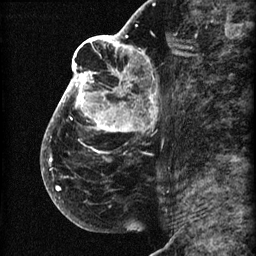
Breast MRI (dynamic contrast-enhanced), one sagittal slice. Slice 38 of 60 in the series (ordered by position). 3 images stored at this slice position (order not interpretable as contrast timing). 1.5 T. TE 4.2 ms, TR 22.7 ms. 2 mm slice thickness. 256 × 256 image matrix, field of view 180 × 180 mm. Female patient, age 48 years. From the clinical record (not read from this slice): setting: breast cancer imaged before/during neoadjuvant chemotherapy; receptor status: triple-negative.
Structures marked on this image (semi-automatically segmented with operator editing):
- analysis volume of interest (the breast-tissue region the enhancement analysis was run in; not a lesion): box from (x=44, y=30) to (x=173, y=207) px
- tumour enhancement mask (voxels above the 90 % enhancement threshold inside the analysis volume of interest): (x=44, y=30)–(x=156, y=191)